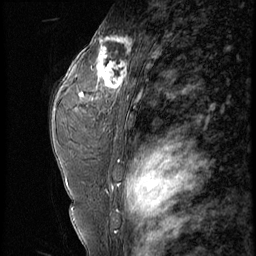
Breast MRI (dynamic contrast-enhanced), one sagittal slice. Slice 38 of 56 in the series (ordered by position). 4 images stored at this slice position (order not interpretable as contrast timing). 1.5 T. TE 4.2 ms, TR 9 ms. 2.5 mm slice thickness. 256 × 256 image matrix, field of view 180 × 180 mm. Patient: female, 44 years. From the clinical record (not read from this slice): setting: breast cancer imaged before/during neoadjuvant chemotherapy; receptor status: triple-negative.
Outlined on this slice (semi-automatic segmentation, software-assisted and operator-edited):
- analysis volume of interest (the breast-tissue region the enhancement analysis was run in; not a lesion): bounding box (x1, y1, x2, y2) in pixels: (87, 28, 132, 99)
- tumour enhancement mask (voxels above the 140 % enhancement threshold inside the analysis volume of interest): (91, 36, 131, 99)